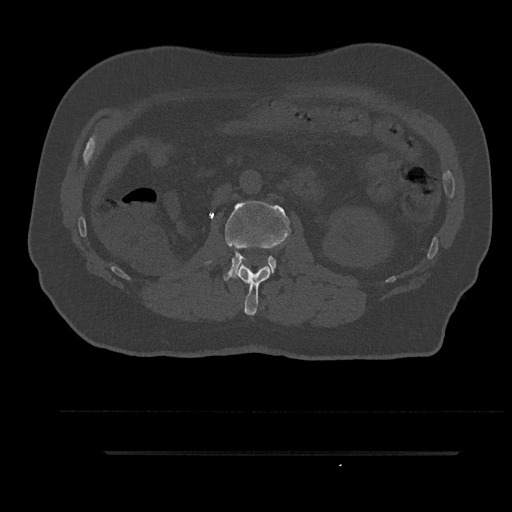
CT including the spine, one axial slice. Position 137 of 797 along the scan axis. Reconstruction kernel Br40s/3. 120 kVp. Bone window (W 1800 / L 400 HU). 0.5 mm slice thickness. 512 × 512 image matrix. Male patient, age 63 years. From the clinical record (not read from this slice): primary cancer: renal; vertebrae with lytic lesions (as recorded): T8.
Annotated regions visible in this slice (semi-automatically segmented with operator editing):
- L1 vertebra: bounding box (x1, y1, x2, y2) in pixels: (235, 264, 271, 316)
- L2 vertebra: (207, 201, 291, 281)